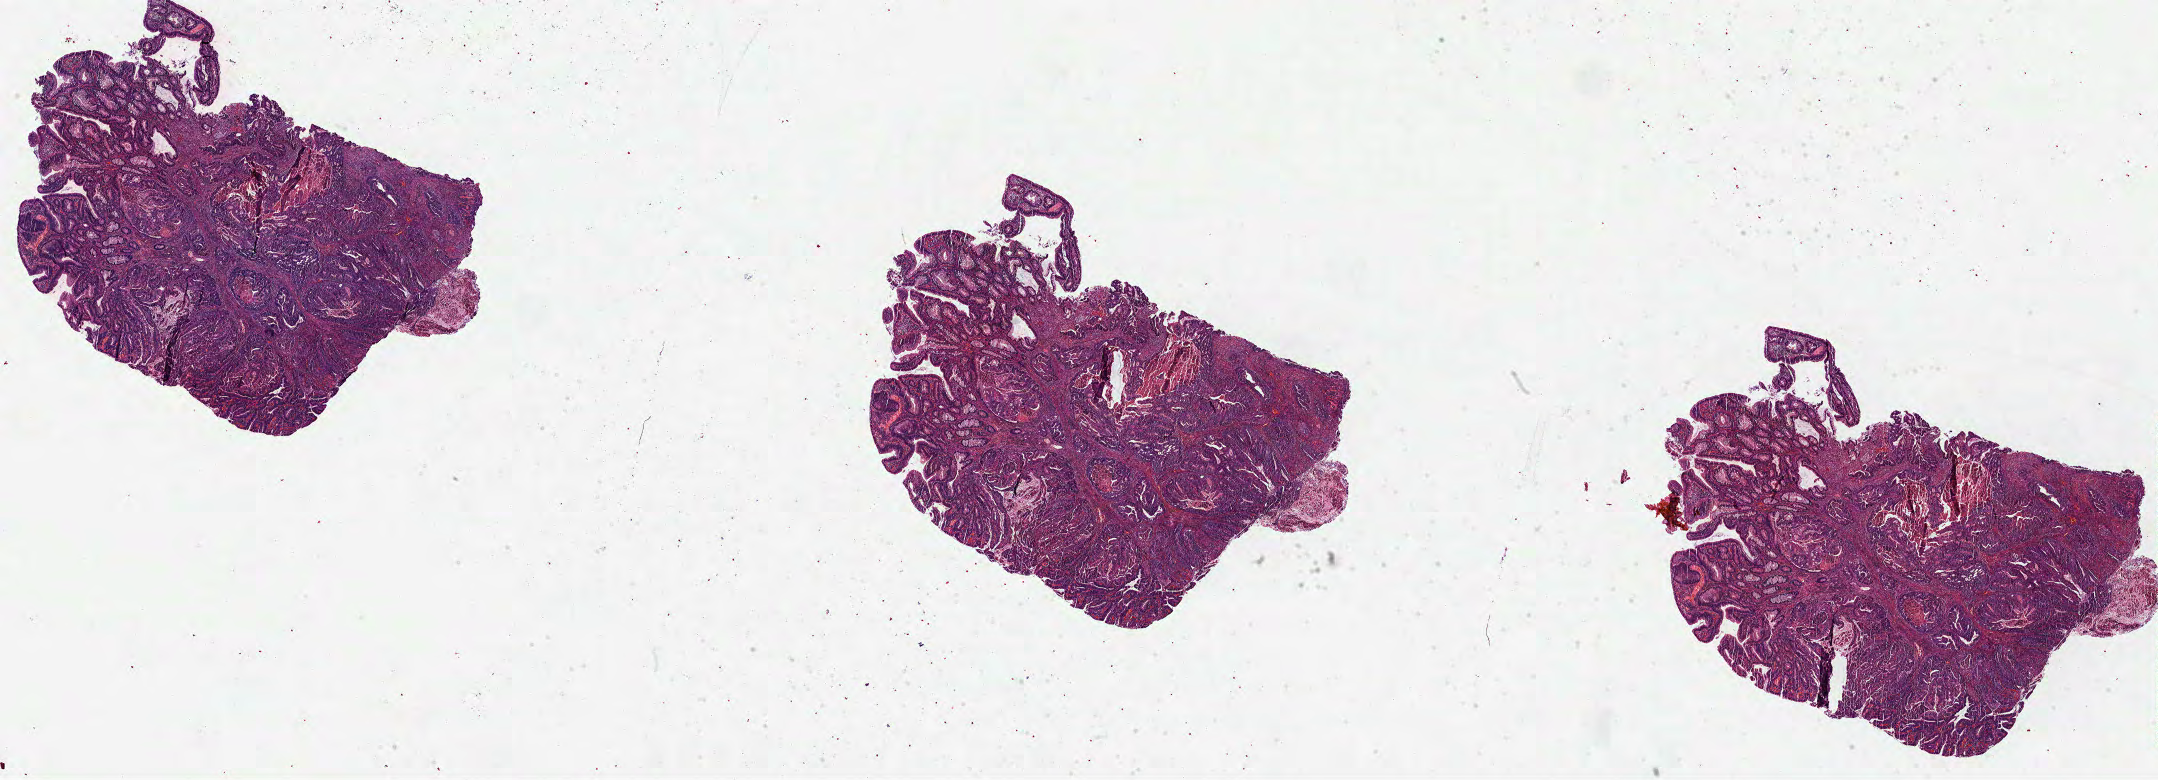
Digitized H&E tissue section (whole slide) — whole scanned area (about 34.8 x 12.6 mm, slide scanned at 40x) shown as a low-resolution overview. Formalin-fixed paraffin-embedded (FFPE) diagnostic section. Primary tumour sample from the colon. Patient: male, age at initial diagnosis 55 years.
Histologic diagnosis: Adenocarcinoma, NOS (ascending colon).